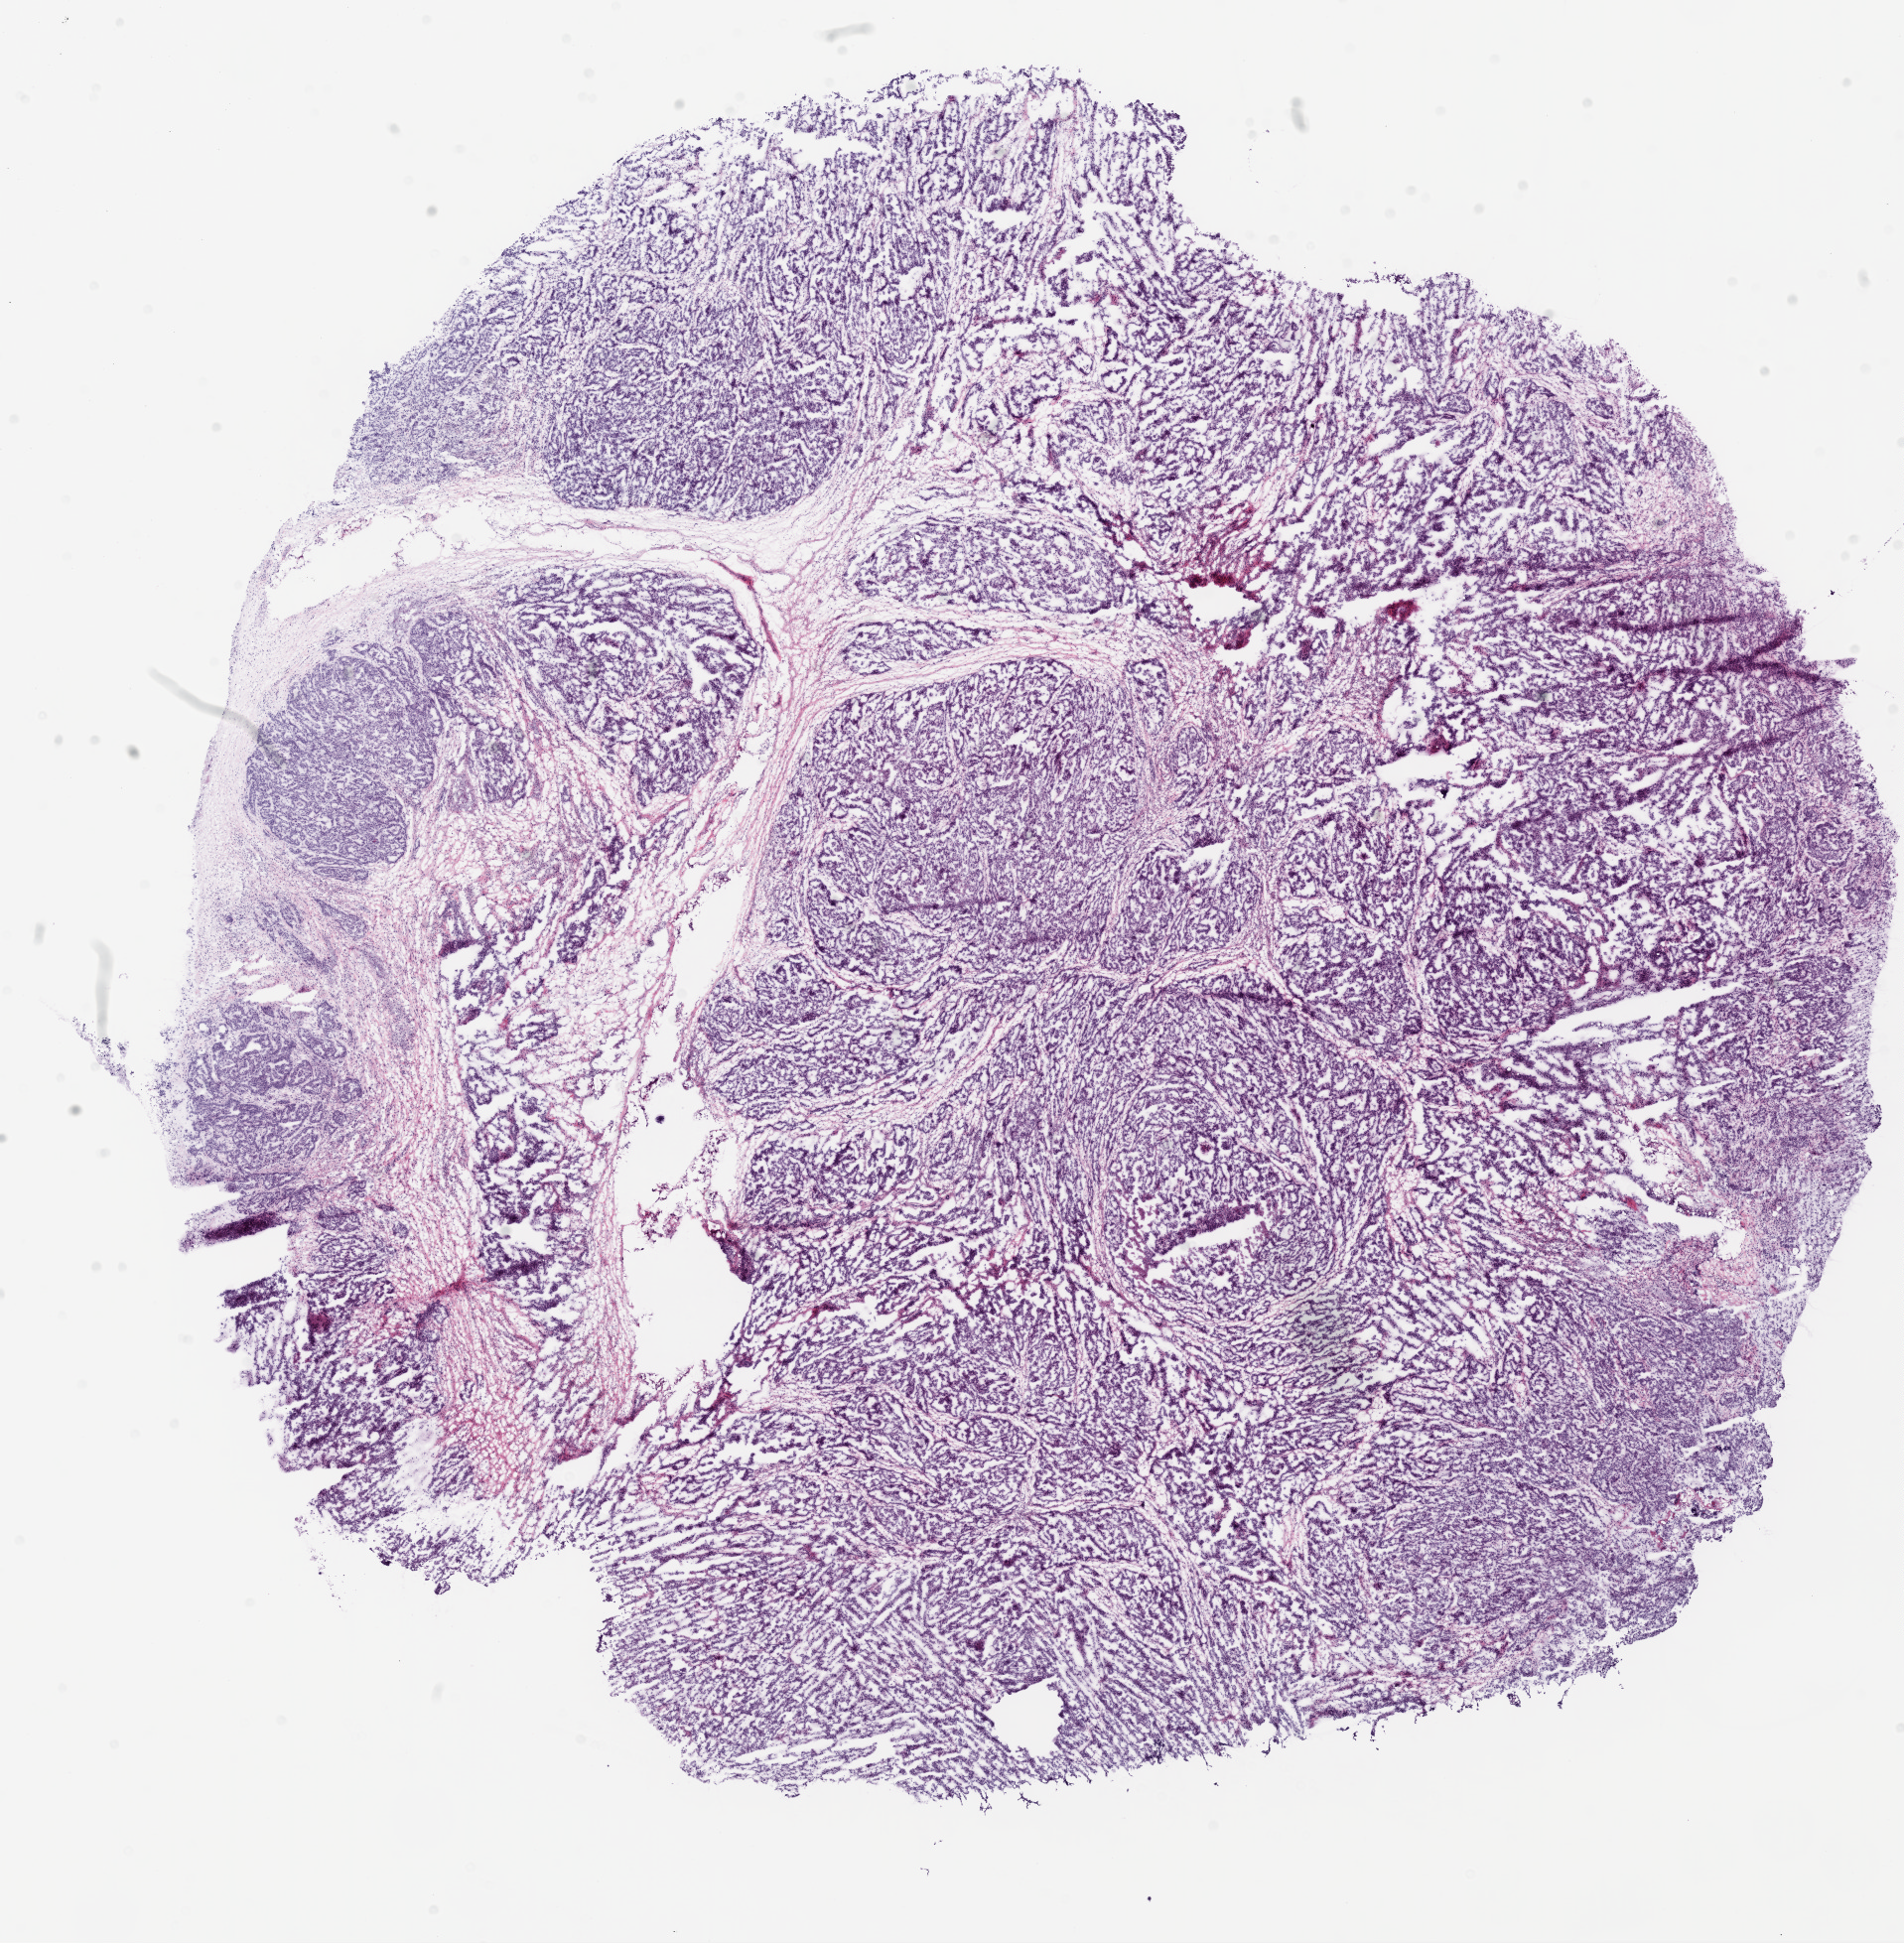
Digitized H&E tissue section (whole slide) — low-resolution overview of the scanned area, about 15.5 x 15.8 mm, frozen section from the top of the tissue portion, ovary, primary tumour sample. Female, age 44 years at initial diagnosis. Slide review estimates, as recorded: tumour cells 90%, tumour nuclei 95%.
Histologic diagnosis: Serous cystadenocarcinoma, NOS.